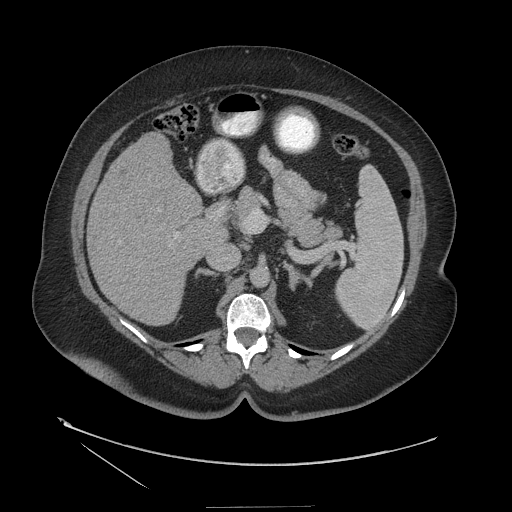
Contrast-enhanced abdominal CT (liver protocol), one axial slice. Position 66 of 127 along the scan axis. Reconstruction kernel STANDARD. 140 kVp. Soft-tissue window (W 400 / L 40 HU). 2.5 mm slice thickness. 512 × 512 image matrix, field of view 480 × 480 mm. From the clinical record (not read from this slice): diagnosis: hepatocellular carcinoma (patient treated with transarterial chemoembolisation; whether this scan precedes or follows treatment is not stated here); TNM stage (as recorded): Stage-II; Child-Pugh class: A; tumour differentiation: well differentiated; tumour size: 3 cm.
Structures marked on this image (semi-automatically segmented with operator editing):
- liver parenchyma outside the tumour (the mass and vessels are separate outlines, so this box may not span the whole liver): bounding box (x1, y1, x2, y2) in pixels: (88, 134, 216, 326)